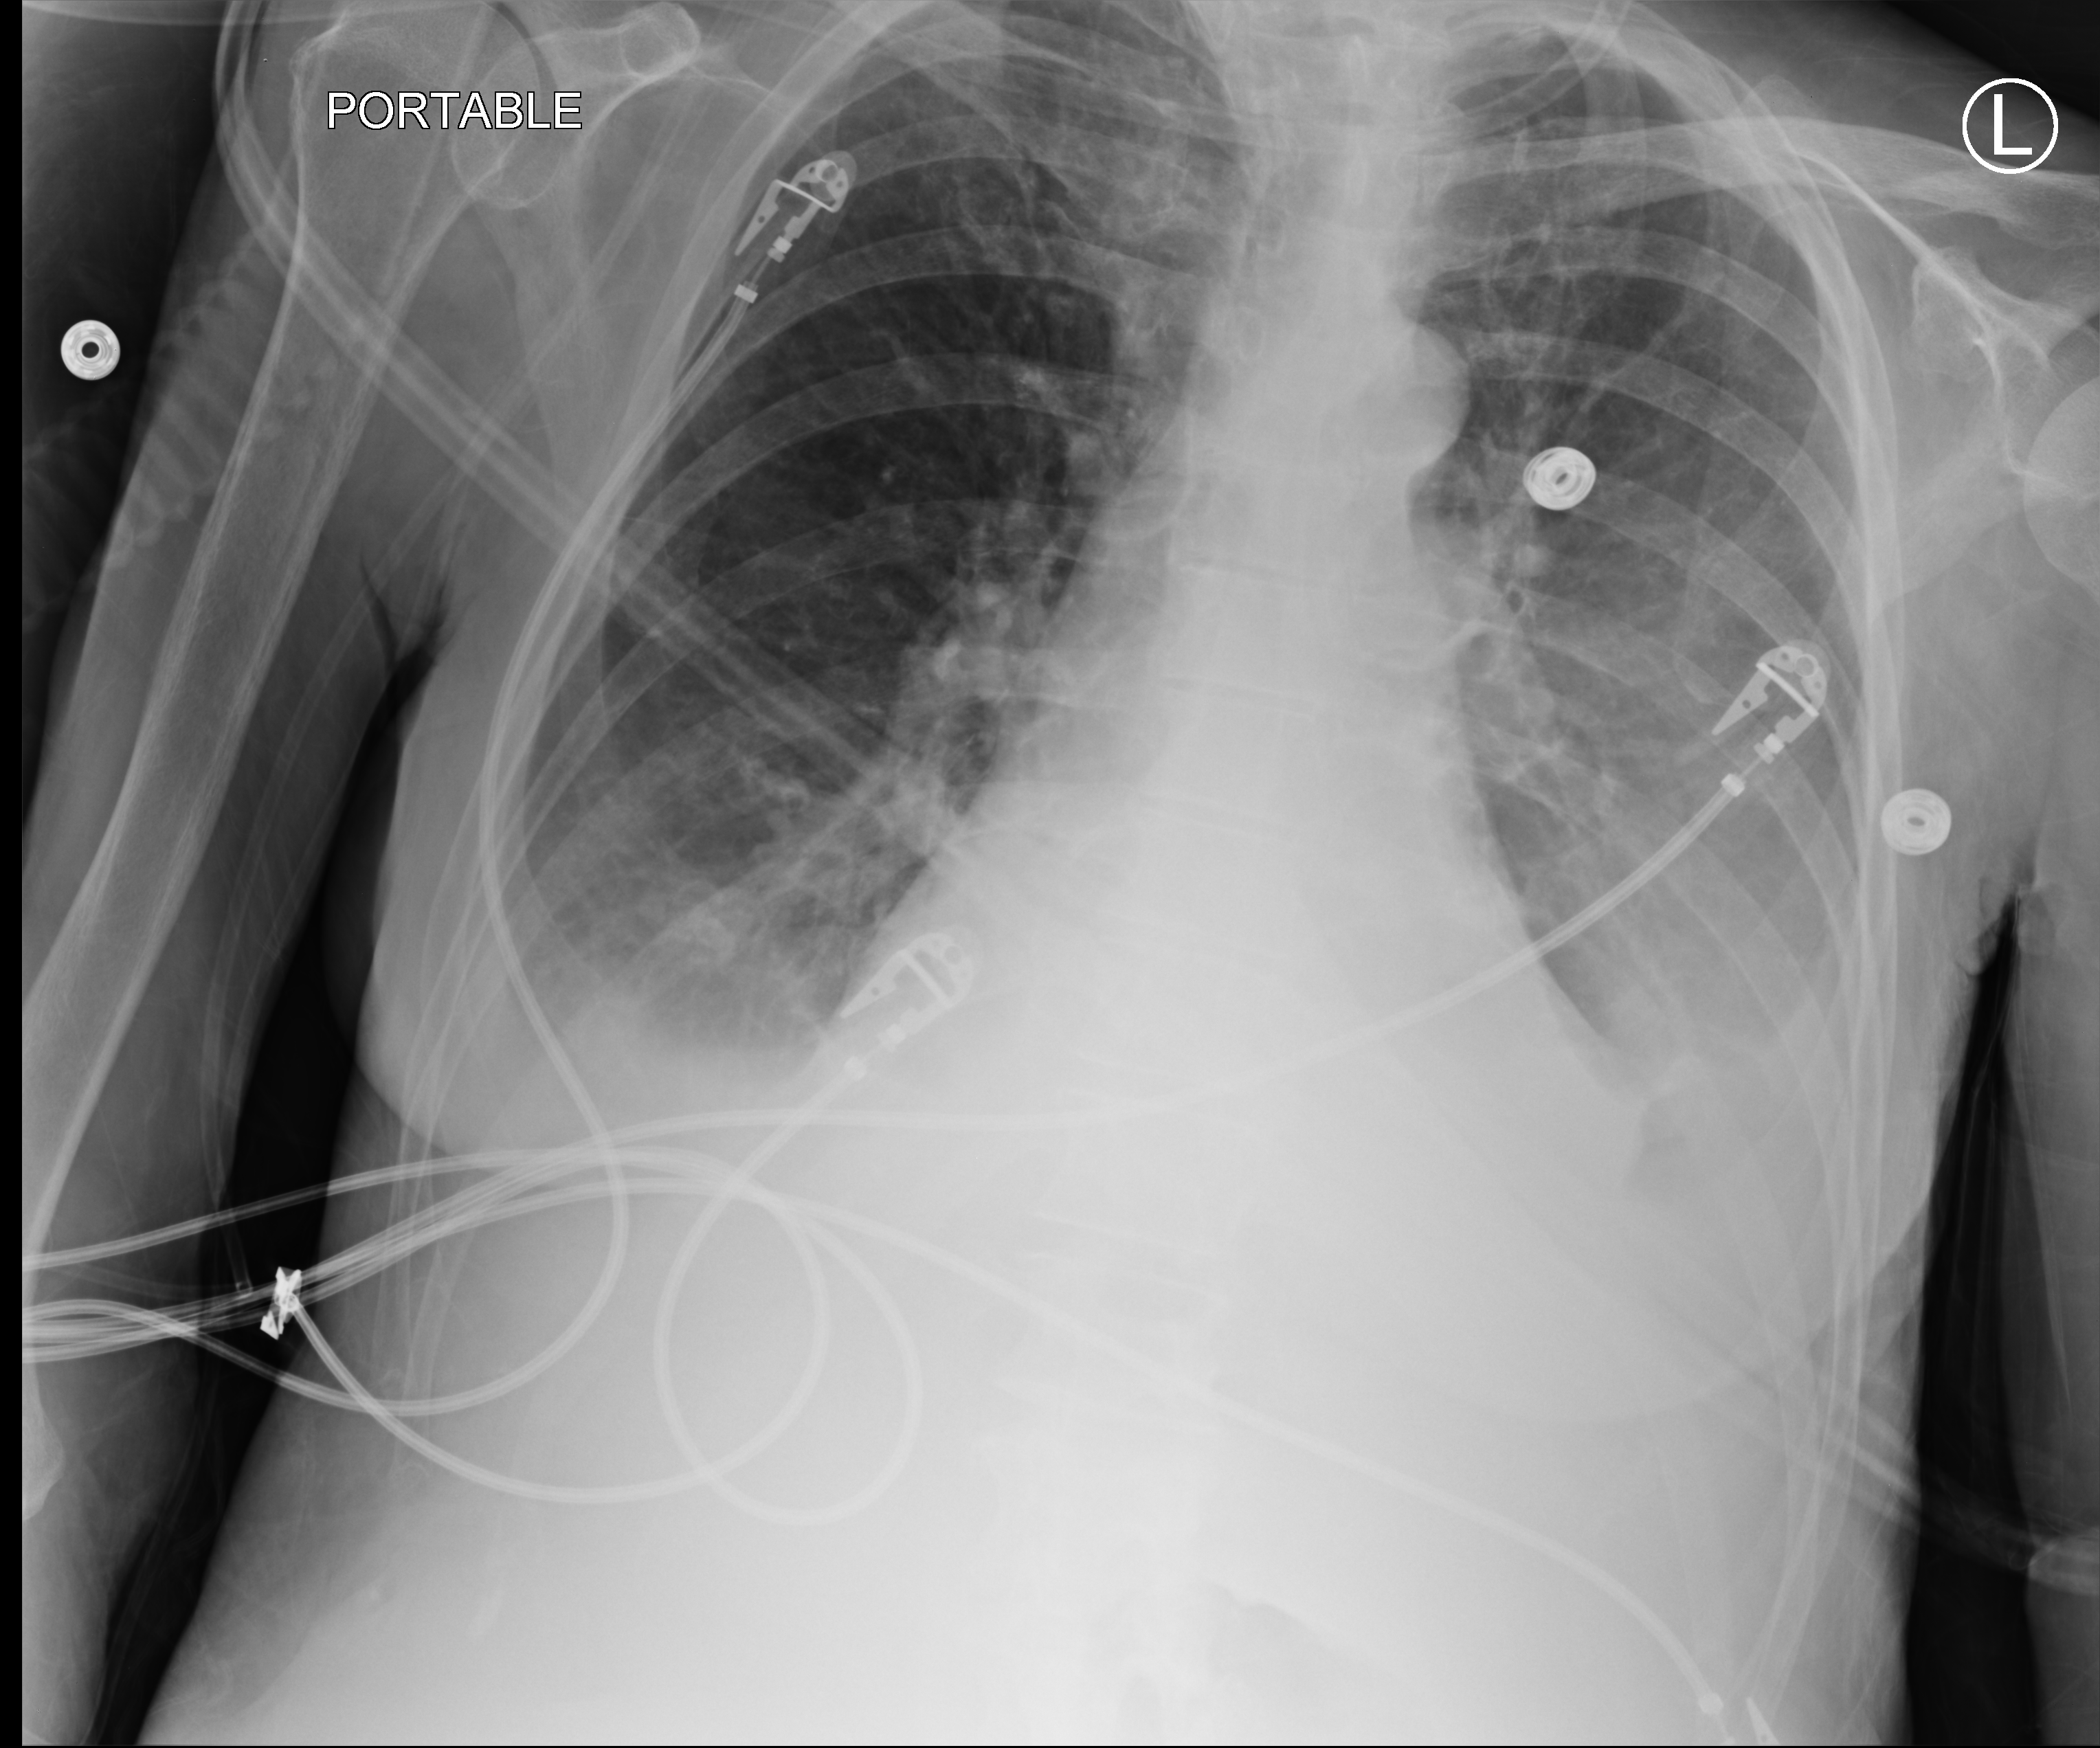
Portable chest radiograph, anteroposterior (AP) projection. Patient hospitalised with COVID-19; female, aged 60–74 years.
Hospital-stay facts (about this admission, not read from this image; timing relative to this image not recorded): mechanically ventilated during this hospital stay: yes; admitted to intensive care during this hospital stay: yes.